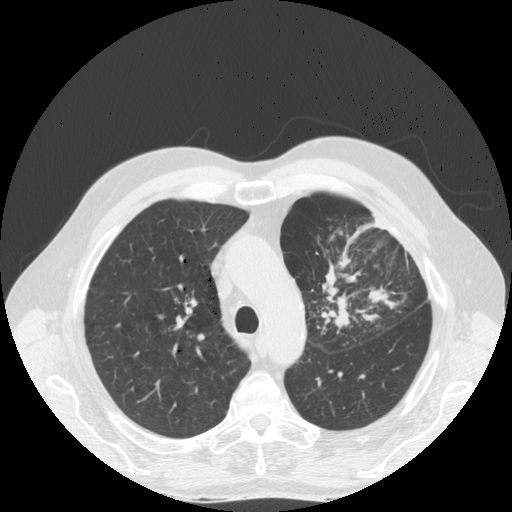
Low-dose screening chest CT, one axial slice; position 126 of 170 along the scan axis; reconstruction kernel STANDARD; lung window (W 1500 / L -600 HU); 2.5 mm slice thickness; 512 × 512 image matrix, field of view 380 × 380 mm.
Annotated regions visible in this slice (expert manual segmentation):
- lesion 1 (tumor, upper lobe of left lung): bounding box [x1, y1, x2, y2] px = [333, 290, 356, 329]